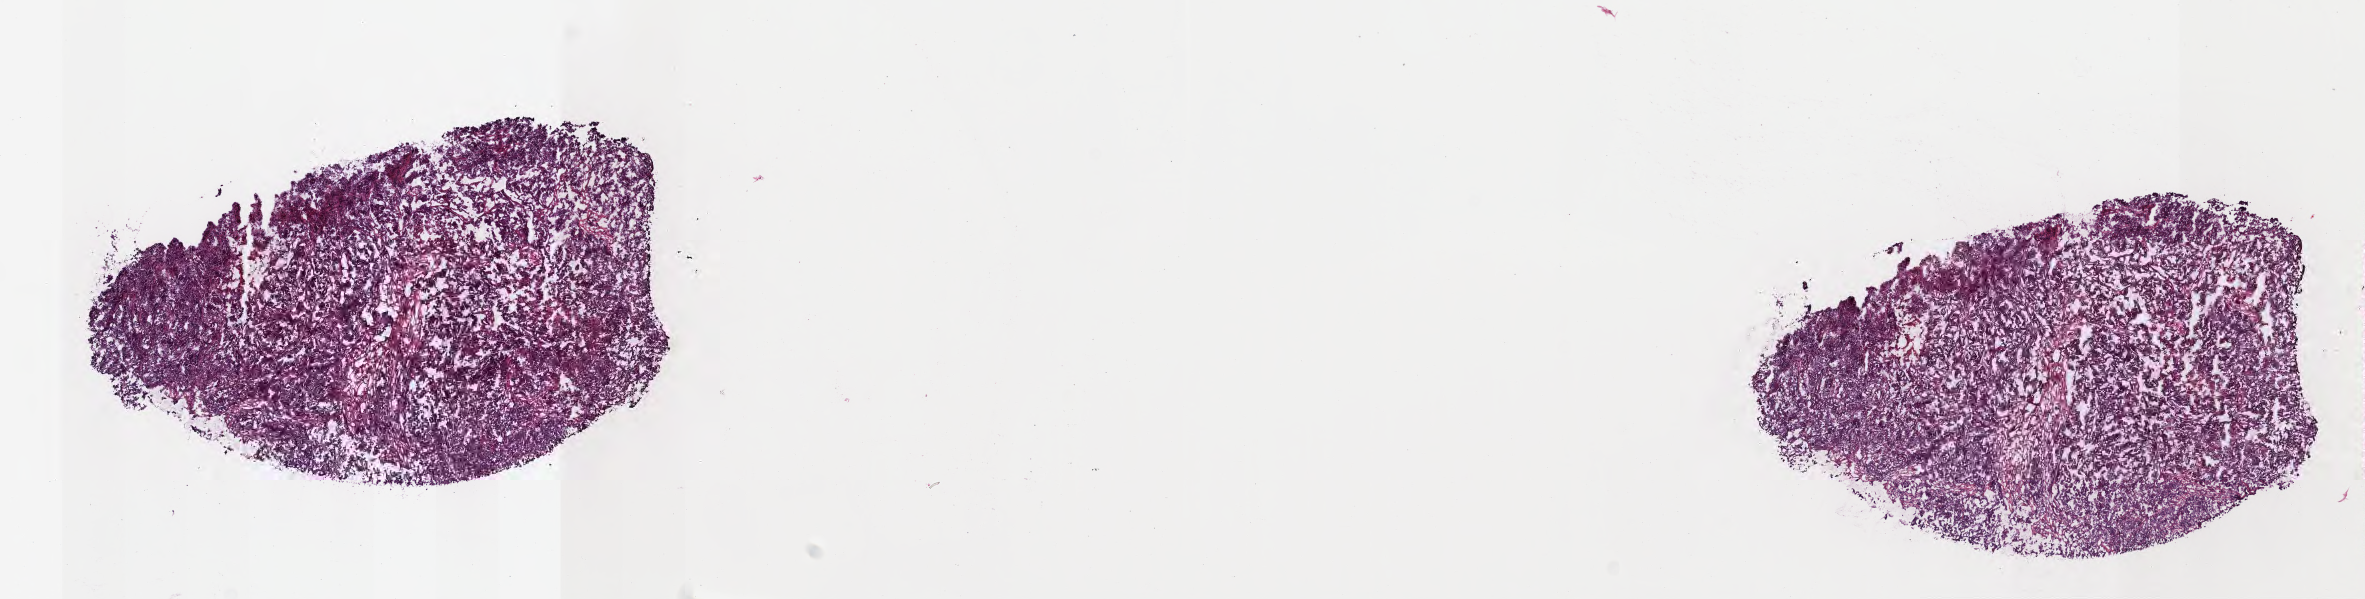
H&E whole-slide image — shown as a low-resolution overview of the whole scanned area (about 19.1 x 4.8 mm); frozen section (tissue freezing medium); metastatic tumor tissue, resected from specified parts of peritoneum. Patient sex: female. Pathologist review of this section (percent, as recorded): tumor cells 100%, tumor nuclei 95%, stromal cells 0%, necrosis 0%, normal cells 0%. Inflammatory infiltration, as recorded: lymphocyte infiltration 0%, monocyte infiltration 0%, neutrophil infiltration 0%.
Patient diagnosis (primary): Adenocarcinoma, metastatic, NOS.